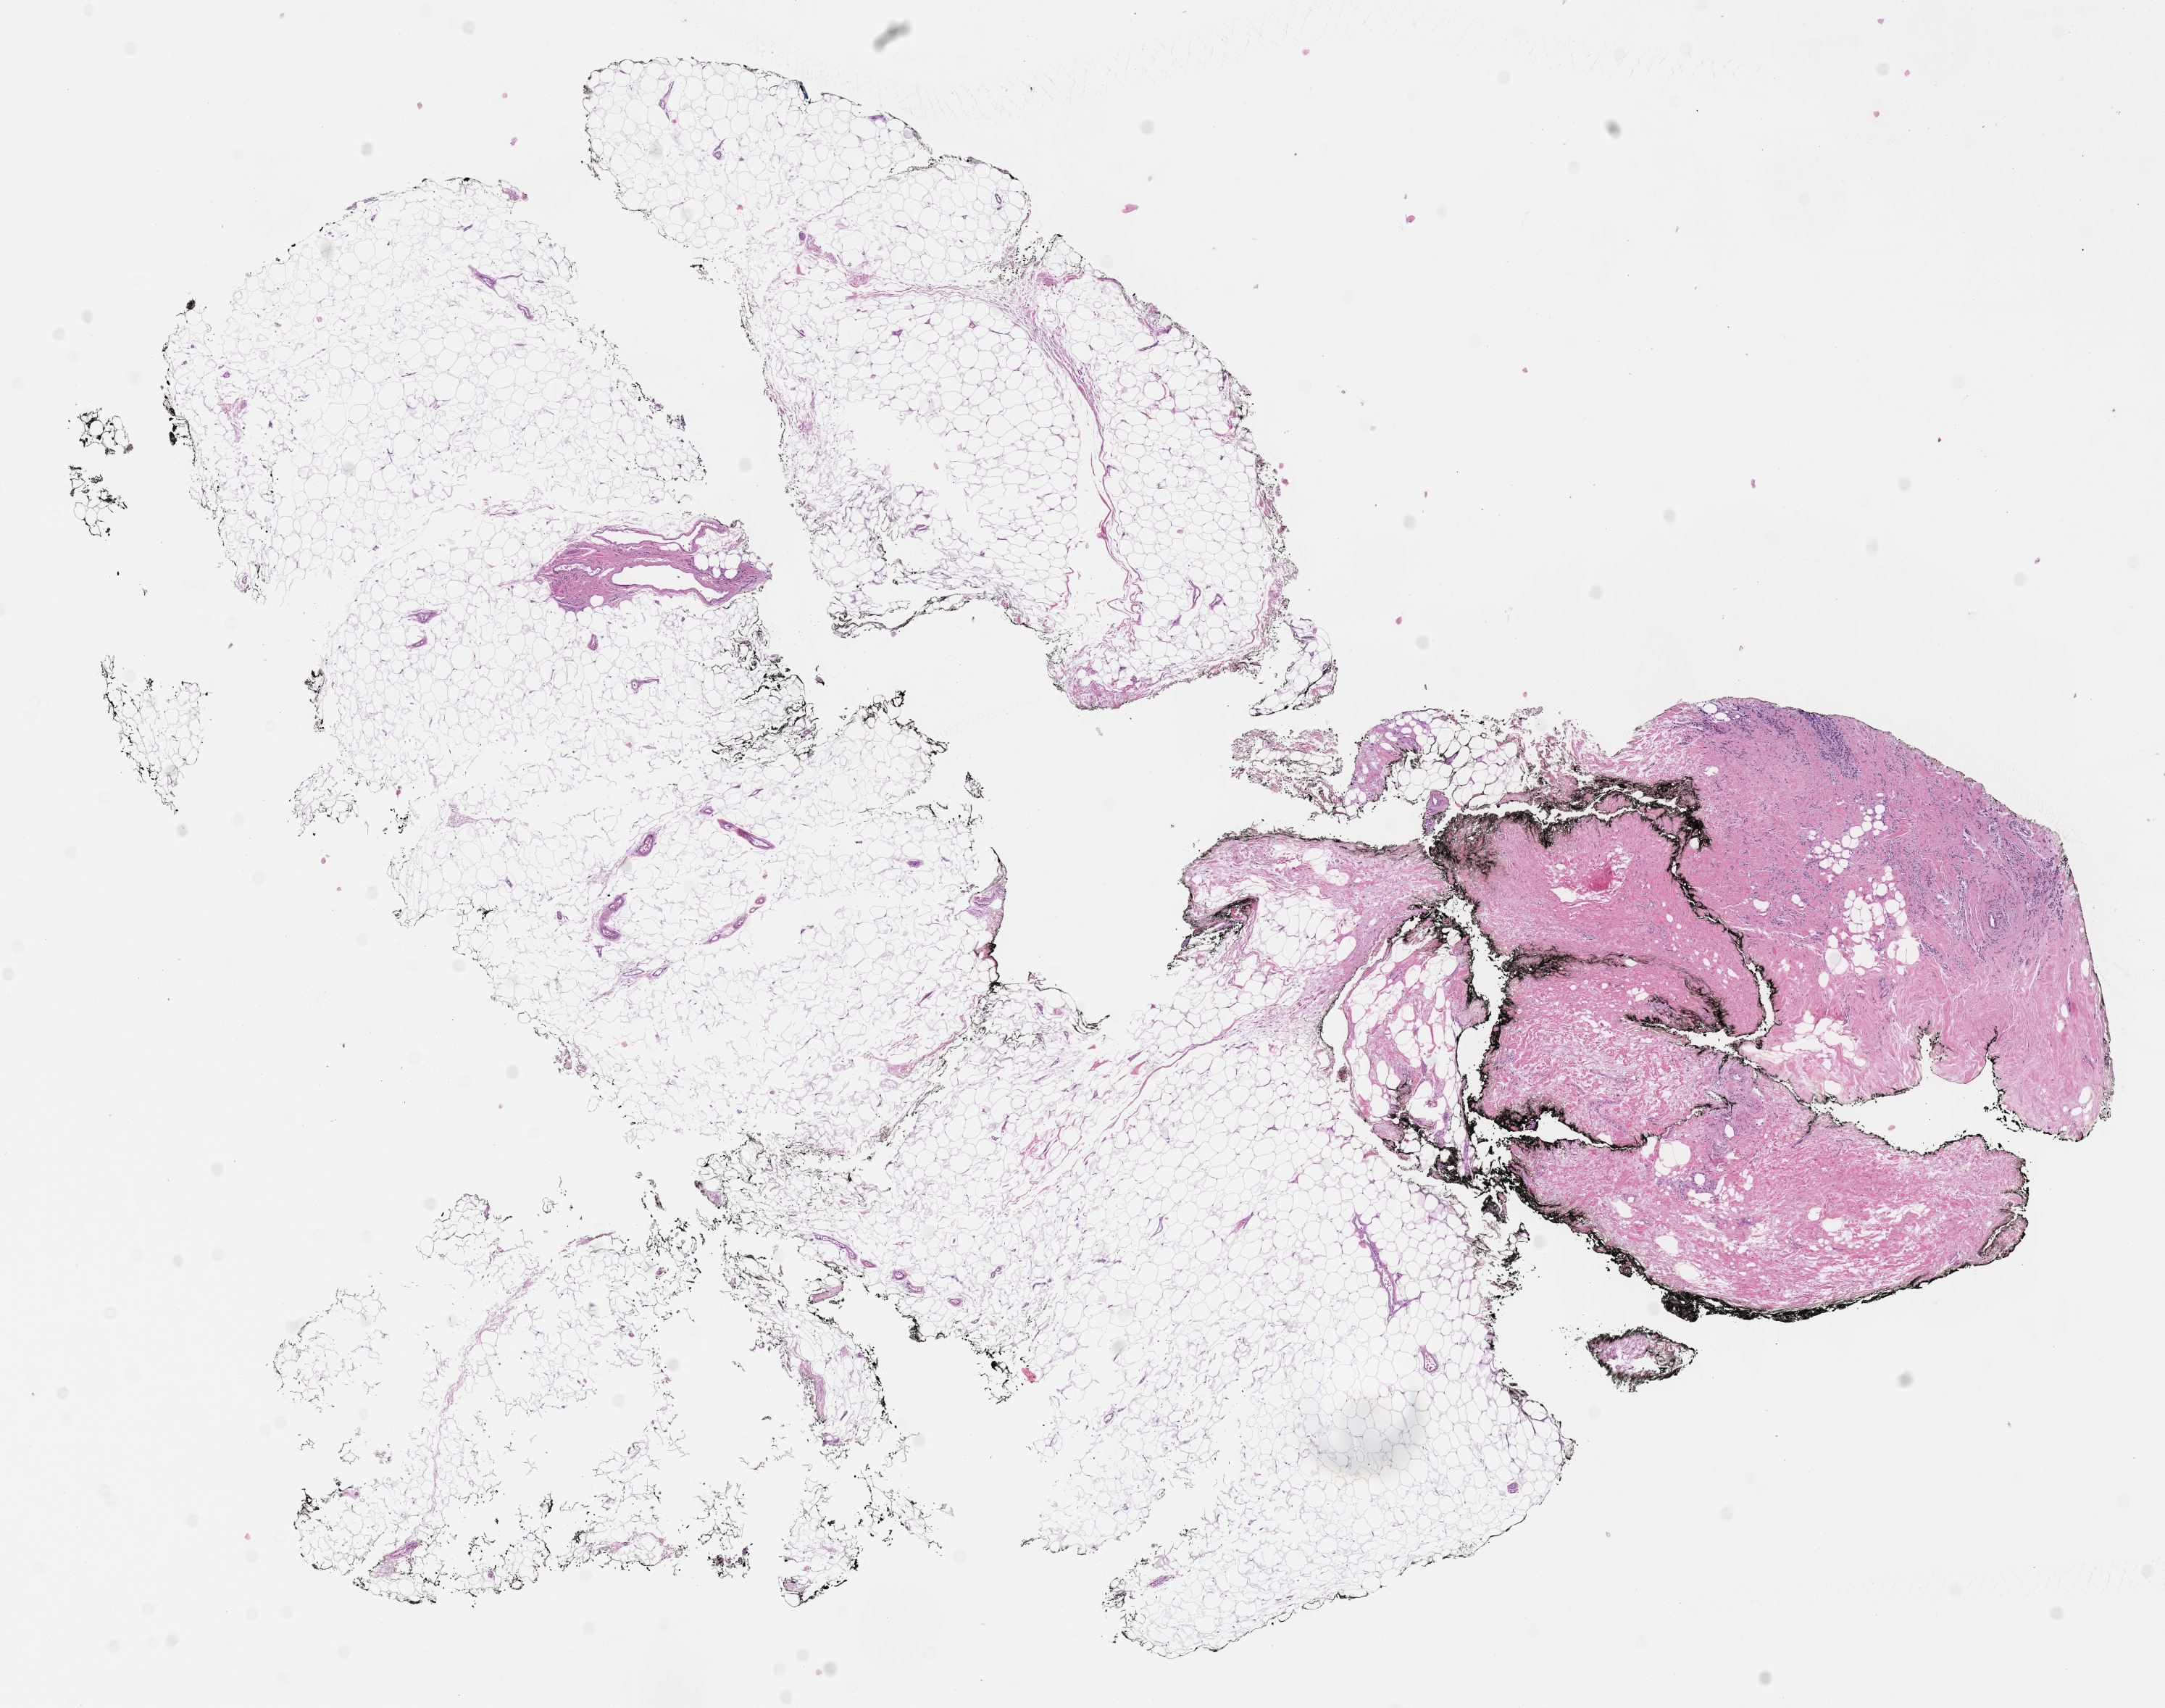
Hematoxylin and eosin (H&E) stained whole-slide image — shown as a low-resolution overview of the whole scanned area (about 11.7 x 9.3 mm, slide scanned at 40x), formalin-fixed paraffin-embedded (FFPE) diagnostic section, sample: primary tumour, breast. Female, age 62 years at initial diagnosis.
Diagnosis: Lobular carcinoma, NOS. AJCC pathologic stage: IIIC (6th edition). Lymph nodes positive (case pathology): 18 of 18 examined.